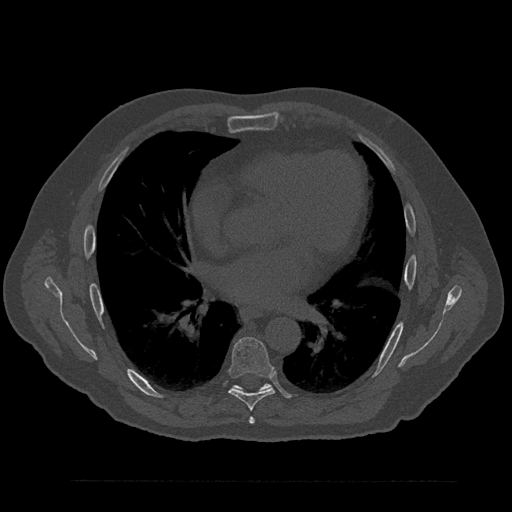
CT including the spine, one axial slice; bone window (W 1800 / L 400 HU); 512 × 512 image matrix. Patient: male, 61 years. Case-level facts recorded for this patient, not image findings: primary cancer: prostate.
Annotated regions visible in this slice (semi-automatic segmentation, software-assisted and operator-edited):
- T6 vertebra: box from (x=249, y=417) to (x=255, y=424) px
- T7 vertebra: (x=228, y=337)–(x=275, y=411)
- T8 vertebra: (x=233, y=383)–(x=271, y=391)